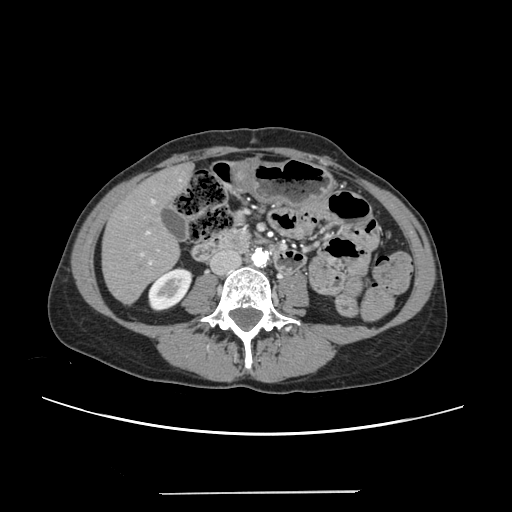
Contrast-enhanced abdominal CT, one axial slice. Slice 71 of 240 in the series (ordered by position). Intravenous contrast given. Soft-tissue window (W 400 / L 40 HU). 512 × 512 image matrix, field of view 371 × 371 mm. Female patient, age 60 years. From the clinical record (not read from this slice): diagnosis: colorectal cancer liver metastases, imaged before liver resection; multiple liver metastases: no.
Outlined on this slice (manually delineated by an expert):
- liver: bounding box <103,166,189,302> (left, top, right, bottom; pixels)
- planned liver remnant (the part of the liver to remain after resection): <103,172,179,302>
- portal vein (with intrahepatic branches): <140,199,156,264>